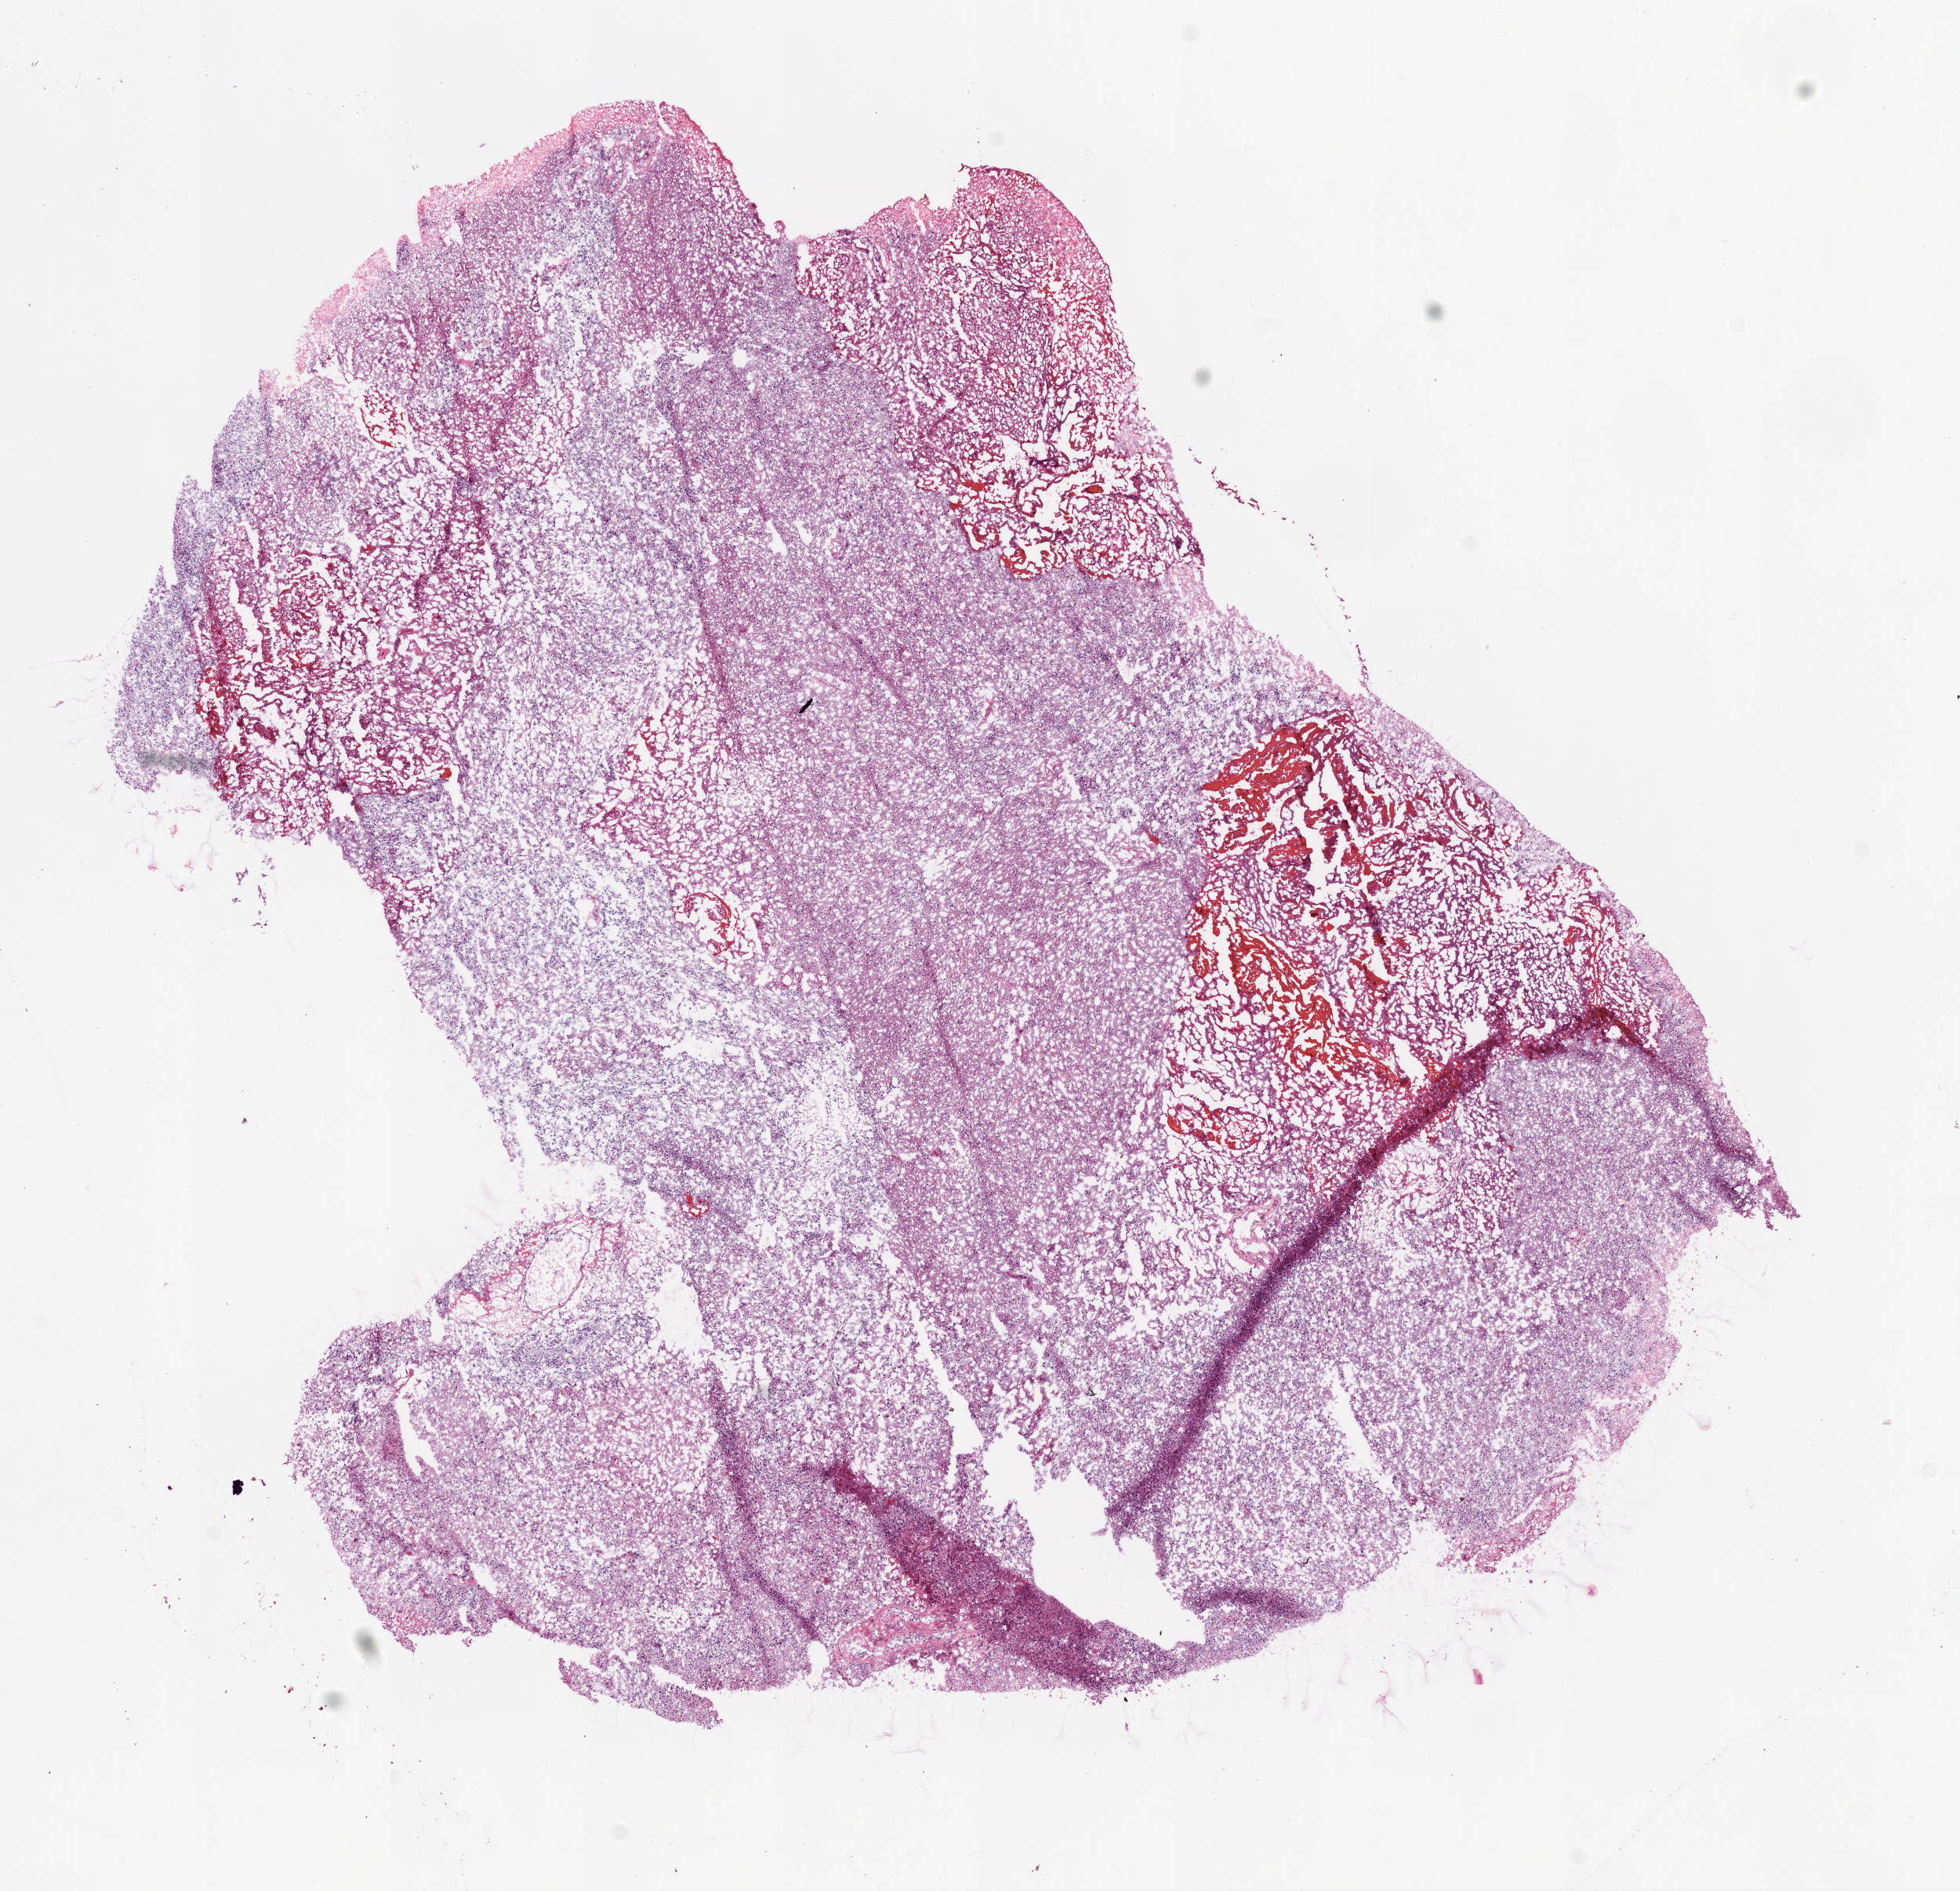
Digitized H&E-stained tissue section (whole slide), whole scanned area (about 10.0 x 9.7 mm, acquisition: 20x scan) shown as a low-resolution overview; frozen section from the bottom of the tissue portion; sample: primary tumour, brain. Male, age 89 years at initial diagnosis. Slide review estimates, as recorded: tumour cells 97%, tumour nuclei 80%, normal cells 0%, stromal cells 0%, necrosis 3%.
Pathologic diagnosis: Glioblastoma.